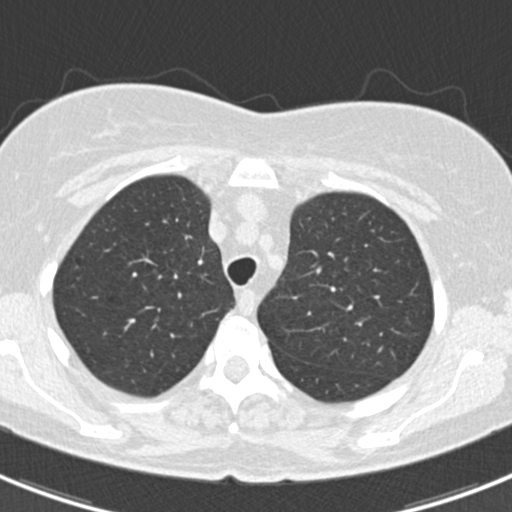
Low-dose screening chest CT, axial slice. Baseline screening round. Lung window (W 1500 / L -600 HU). 2 mm slice thickness. Standard (soft-tissue) reconstruction kernel (B30f). Slice 46 of 184 in the series. Female, age 60 years at enrolment. Current smoker at enrolment.
Lesion marked by an expert reader, bounding box (x1, y1, x2, y2) in pixels: (387, 302, 429, 341). The screening reader recorded 3 non-calcified nodules or masses ≥4 mm on this exam; which of them this box marks is not recorded. Official screen result: positive, change unspecified: nodule(s) >= 4 mm or enlarging nodule(s), mass(es), or other non-specific abnormalities suspicious for lung cancer. Later outcome: lung cancer diagnosed 886 days after this screen (after the third annual screen) — non-small cell carcinoma, left upper lobe, poorly differentiated (G3), stage IB (AJCC 6th edition), 7 mm at pathology.